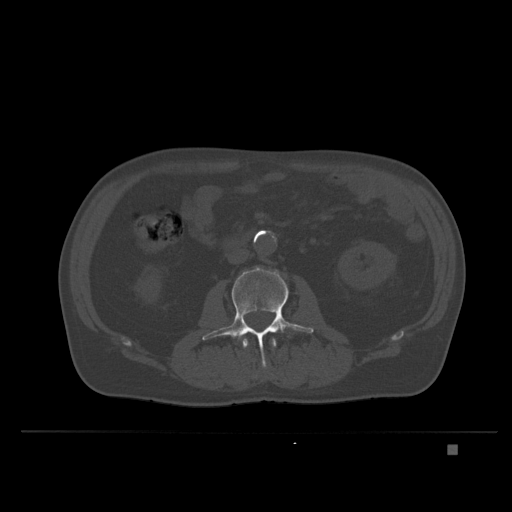
CT including the spine, one axial slice; position 99 of 435 along the scan axis; bone window (W 1800 / L 400 HU); 1.5 mm slice thickness; 512 × 512 image matrix. Patient: male, 73 years. From the clinical record (not read from this slice): primary cancer: skin.
Structures marked on this image (semi-automatic segmentation, software-assisted and operator-edited):
- L2 vertebra: bounding box (x1, y1, x2, y2) in pixels: (243, 338, 277, 378)
- L3 vertebra: (202, 267, 314, 366)